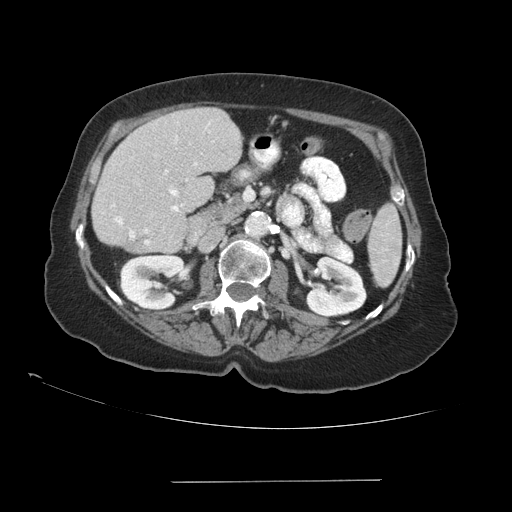
Contrast-enhanced abdominal CT (liver protocol), one axial slice; slice 41 of 89 in the series (ordered by position); reconstruction kernel STANDARD; 140 kVp; soft-tissue window (W 400 / L 40 HU); 2.5 mm slice thickness; 512 × 512 image matrix, field of view 400 × 400 mm. Case-level facts recorded for this patient, not image findings: diagnosis: hepatocellular carcinoma (patient treated with transarterial chemoembolisation; whether this scan precedes or follows treatment is not stated here); TNM stage (as recorded): Stage-IVA; Child-Pugh class: A; tumour differentiation: poorly differentiated; tumour nodularity: uninodular.
Annotated regions visible in this slice (semi-automatic segmentation, software-assisted and operator-edited):
- liver parenchyma outside the tumour (the mass and vessels are separate outlines, so this box may not span the whole liver): box from (x=92, y=108) to (x=242, y=252) px
- liver vessels: (x=112, y=123)–(x=210, y=245)